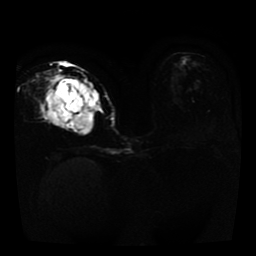
Breast MRI, one axial slice. Slice 19 of 41 in the series (ordered by position). Diffusion-weighted series; image 2 of 4 stored at this slice position (different b-values; order by instance number). 1.5 T. 5 mm slice thickness. 256 × 256 image matrix, field of view 330 × 330 mm. Female patient.
Structures marked on this image (manually delineated by an expert):
- tumour on diffusion-weighted imaging: bounding box (x1, y1, x2, y2) in pixels: (46, 76, 100, 133)